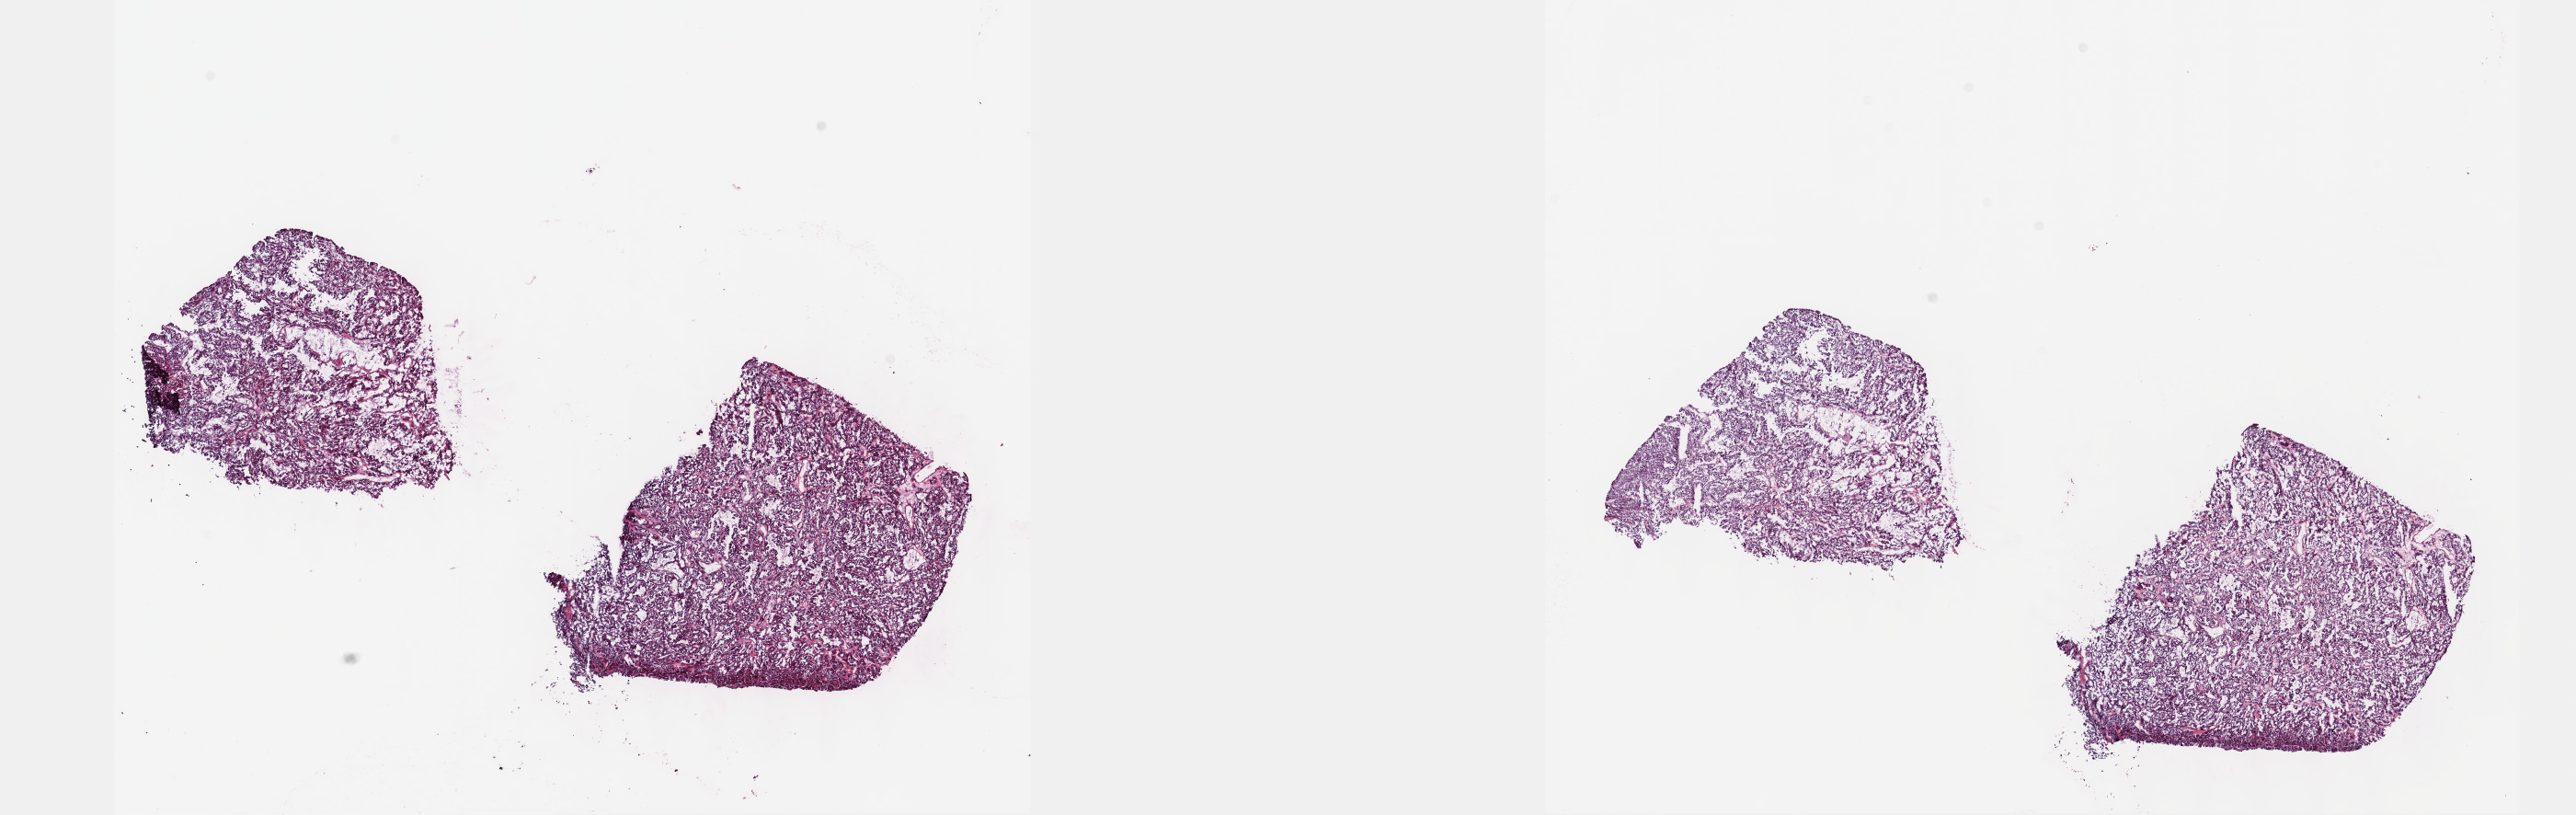
Whole-slide histology image, H&E-stained — a low-resolution overview of the entire scanned area, about 22.6 x 7.2 mm. Frozen section from the top of the tissue portion. Sample: primary tumour, kidney. Patient: male, age at initial diagnosis 64 years. Composition of this section per pathologist review: tumour cells 100%, tumour nuclei 80%, normal cells 0%, stromal cells 0%, necrosis 0%. Inflammatory infiltration, as recorded: lymphocyte infiltration 1%, monocyte infiltration 1%, neutrophil infiltration 0%.
Diagnosis: Papillary adenocarcinoma, NOS. AJCC pathologic stage: I (7th edition). TNM: T1b NX M0.